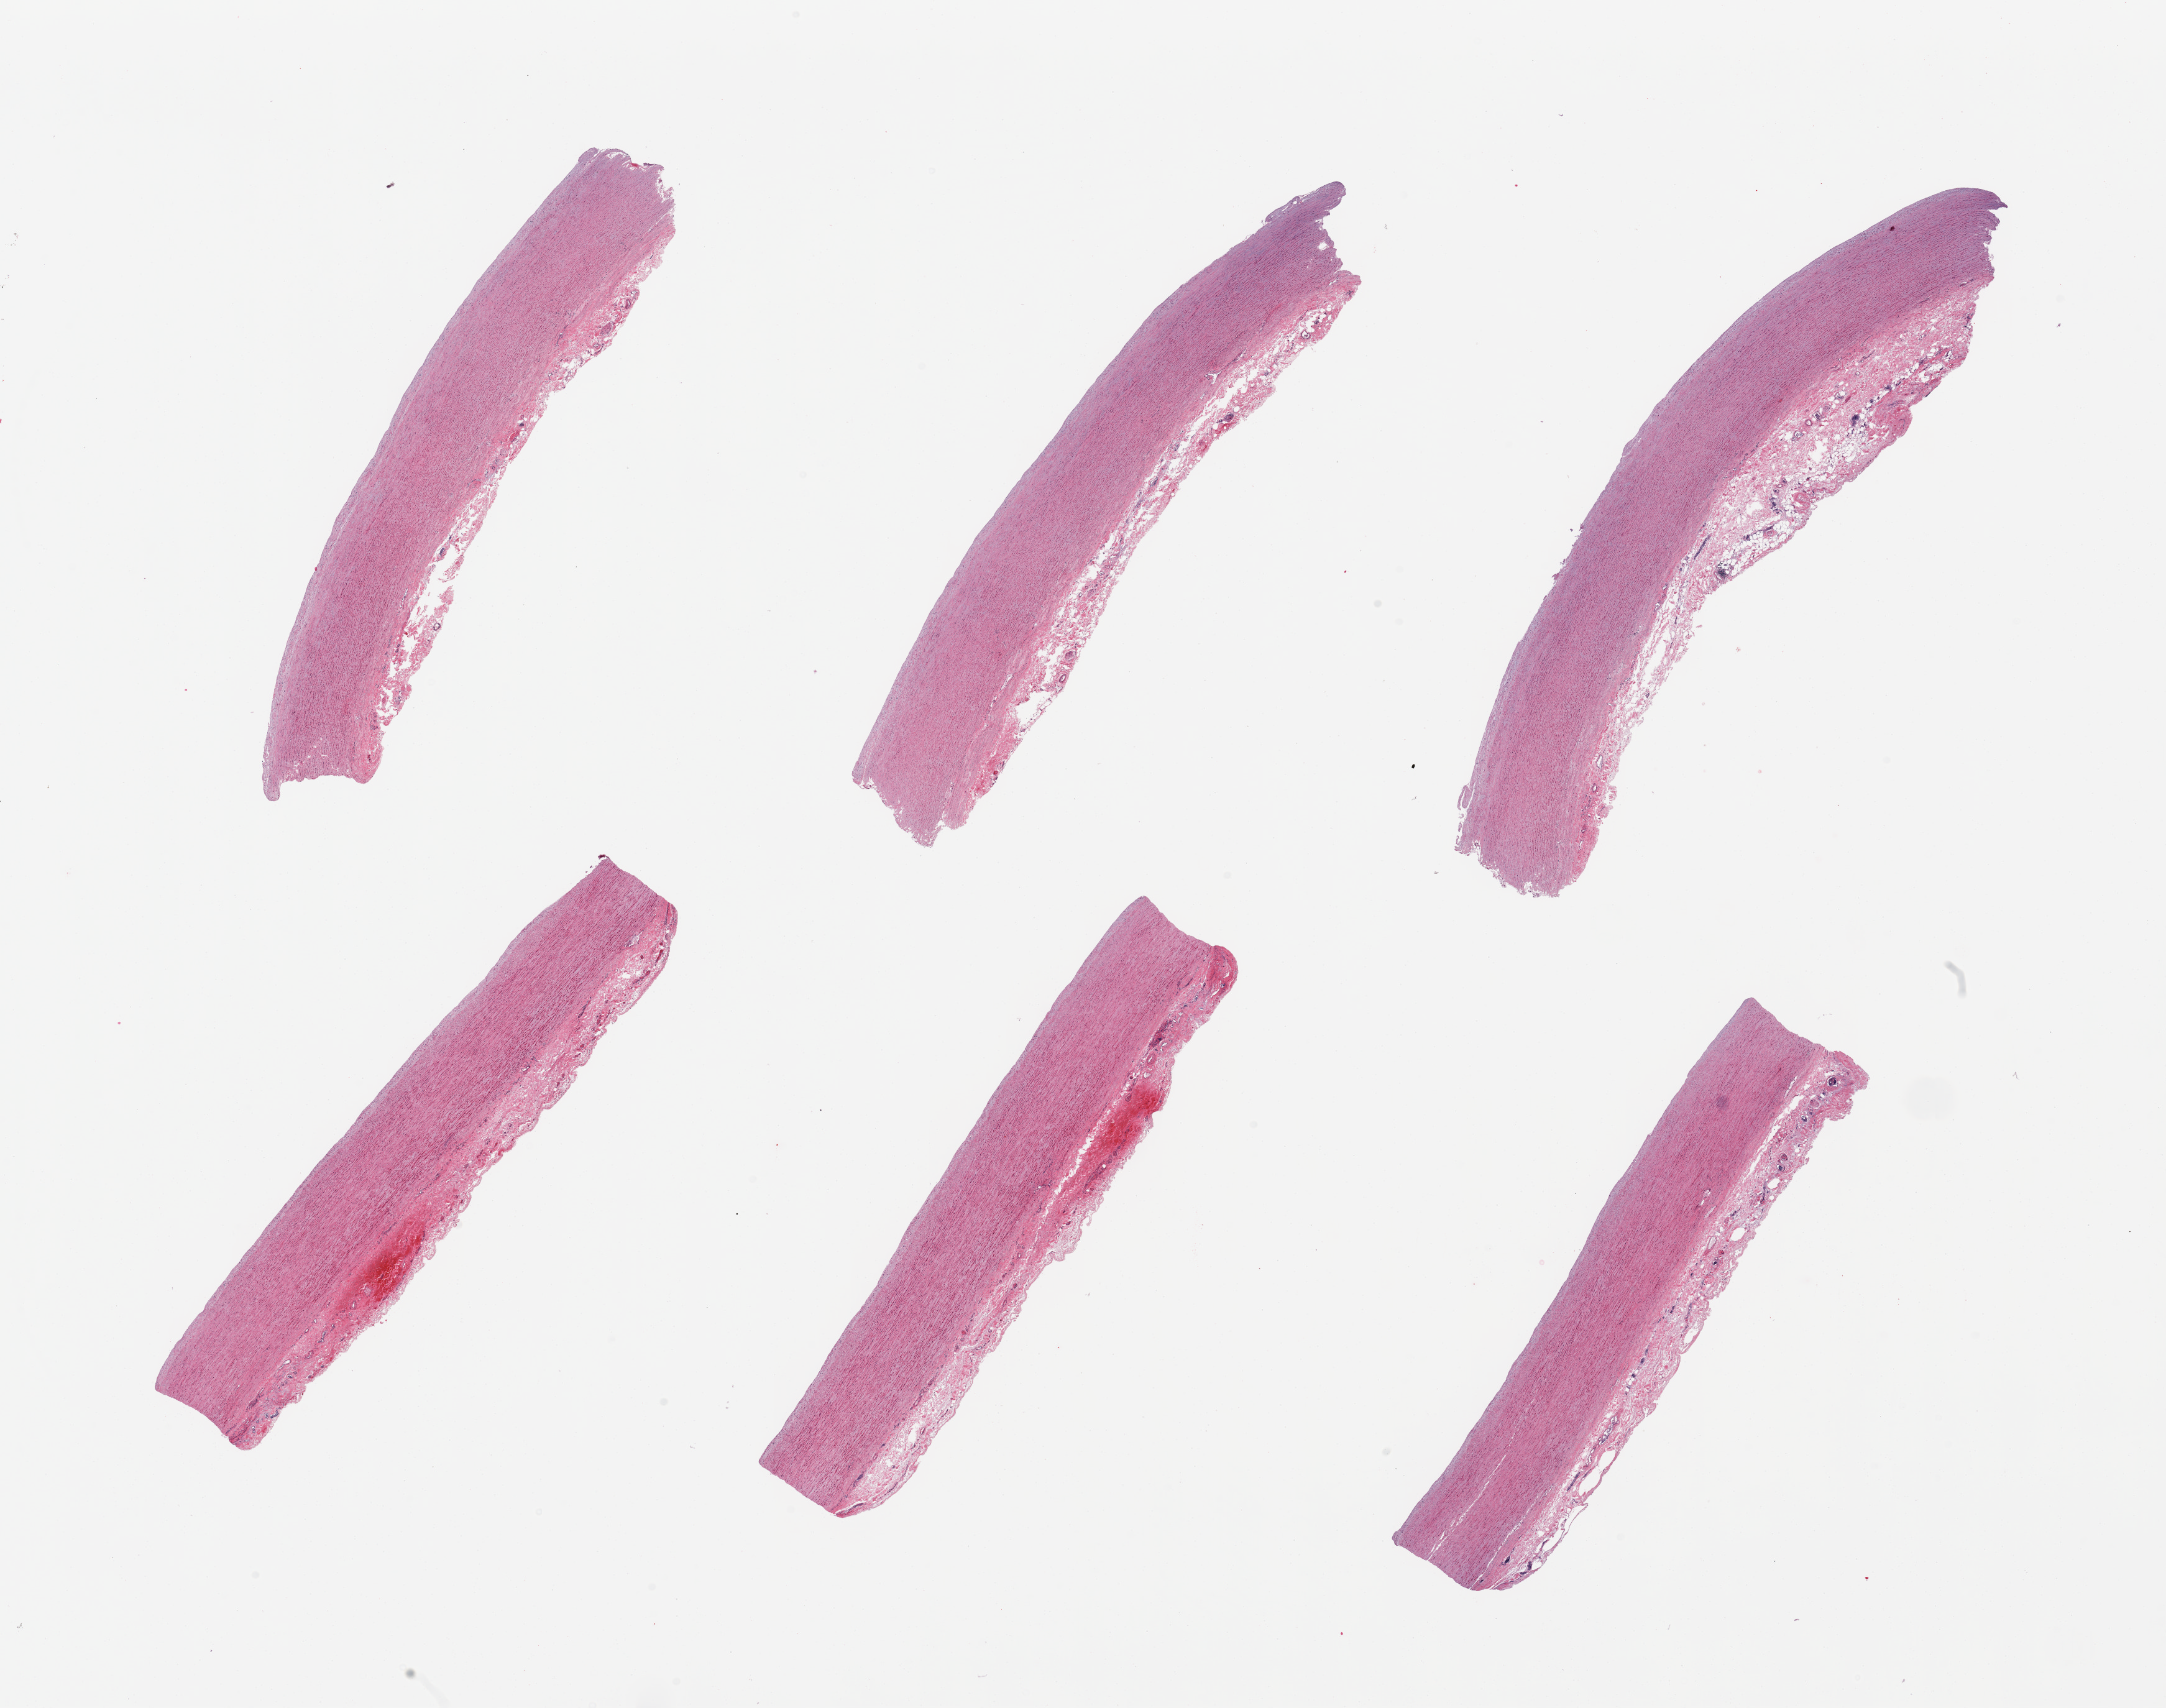
H&E whole-slide image, brightfield, low-resolution overview of the scanned area, about 27.6 x 21.7 mm (slide scanned at 20x). PAXgene-fixed paraffin-embedded (PFPE) section. Sampled site (target tissue): aorta. Tissue donor sample.
Review note (as recorded): 6 pieces, minimal atherosis.